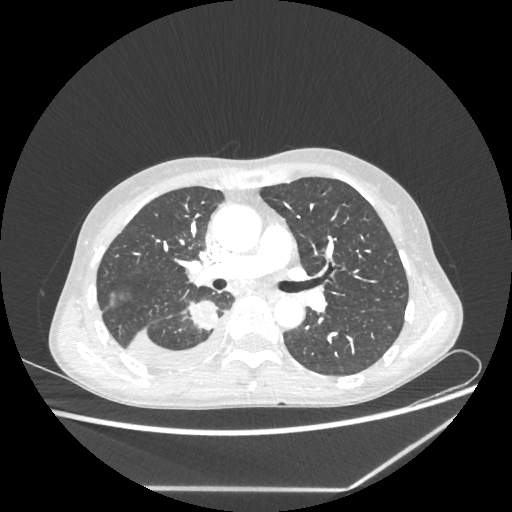
Chest CT, one axial slice; position 137 of 237 along the scan axis; 80 kVp; lung window (W 1500 / L -600 HU); 1.25 mm slice thickness; 512 × 512 image matrix. Patient: female, 59 years. From the clinical record (not read from this slice): clinical TNM (as recorded): T1c N1 M1.
Annotated regions visible in this slice (rectangle marked by the reading radiologist):
- lung tumour (recorded histology: adenocarcinoma): bounding box (x1, y1, x2, y2) in pixels: (185, 300, 220, 333)